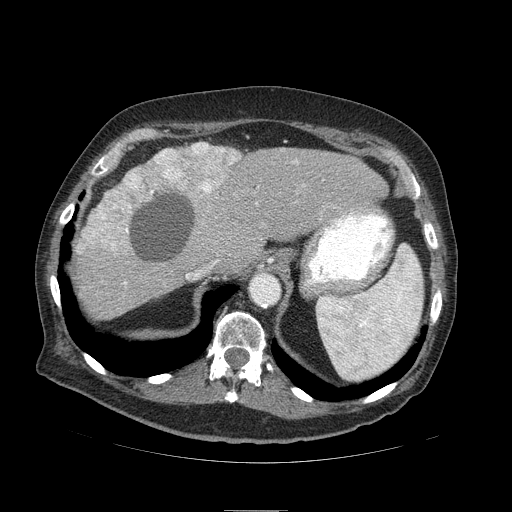
Contrast-enhanced abdominal CT (liver protocol), one axial slice; position 70 of 103 along the scan axis; 120 kVp; soft-tissue window (W 400 / L 40 HU); 512 × 512 image matrix. Case-level facts recorded for this patient, not image findings: diagnosis: hepatocellular carcinoma (patient treated with transarterial chemoembolisation; whether this scan precedes or follows treatment is not stated here); TNM stage (as recorded): Stage-IIIA; Child-Pugh class: B; tumour nodularity: multinodular; tumour size: 13 cm.
Structures marked on this image (semi-automatically segmented with operator editing):
- liver parenchyma outside the tumour (the mass and vessels are separate outlines, so this box may not span the whole liver): bounding box (x1, y1, x2, y2) in pixels: (72, 142, 388, 318)
- mass: (83, 143, 240, 260)
- liver vessels: (186, 274, 189, 278)